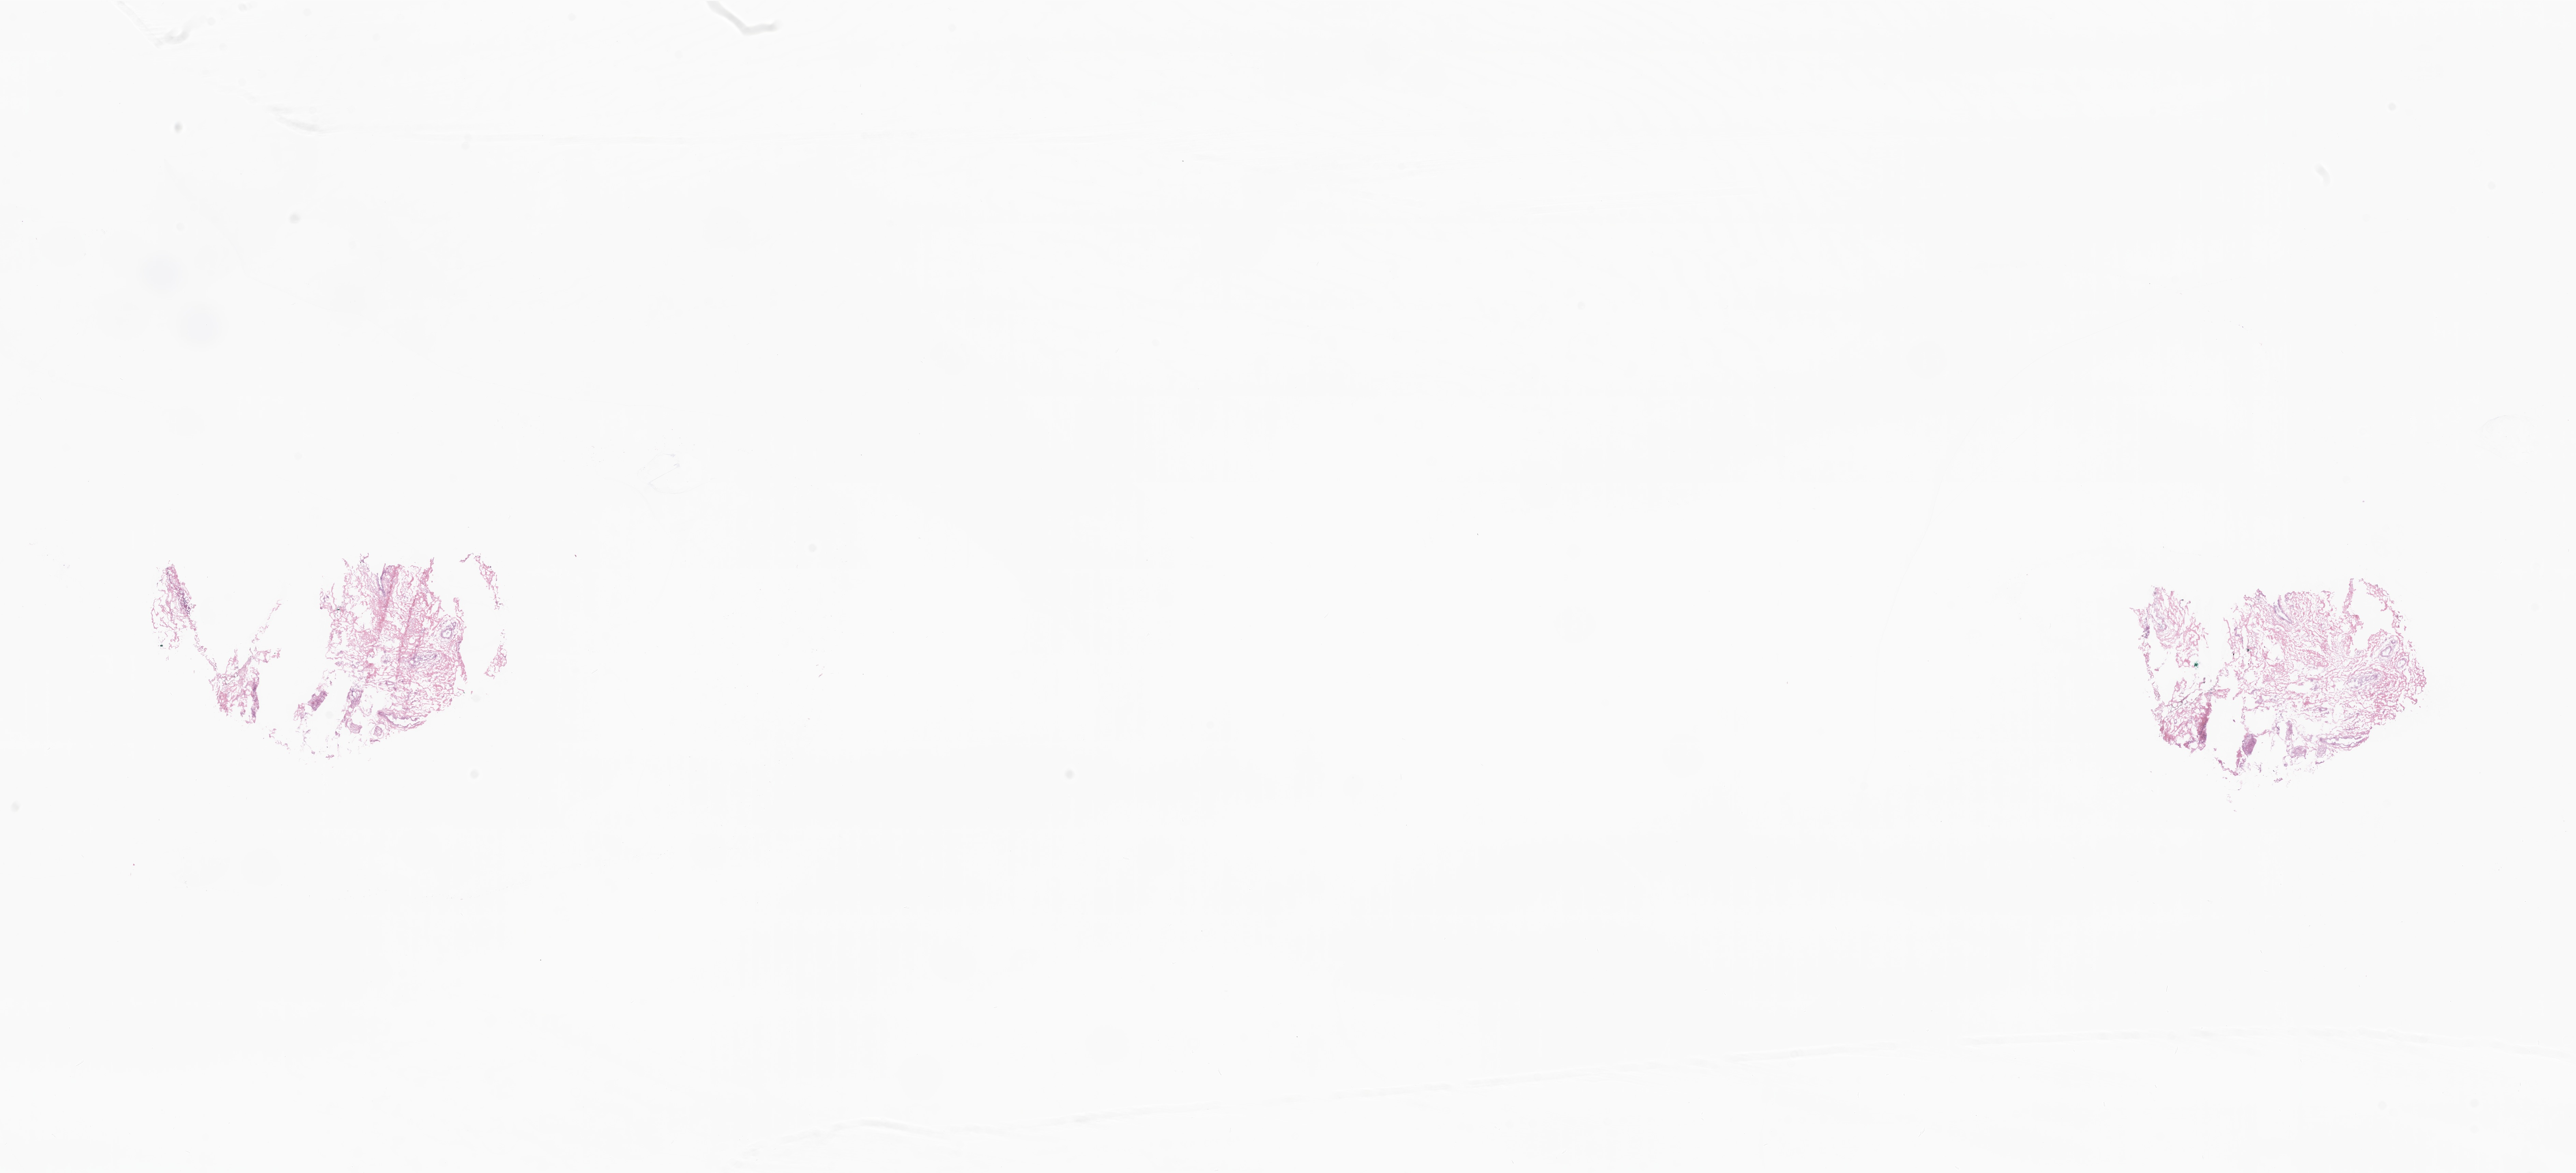
Digitized H&E-stained section — a low-resolution overview of the entire scanned area, about 31.8 x 14.5 mm; frozen section; primary tumor; anatomic site: breast (right). Female patient; age at initial diagnosis 79 years. Pathologist review of this section (percent, as recorded): tumor cells 0%, tumor nuclei 0%, stromal cells 5%, necrosis 0%, normal cells 95%. Inflammatory infiltration, as recorded: lymphocyte infiltration 0%, monocyte infiltration 0%, neutrophil infiltration 0%.
Diagnosis: Infiltrating duct carcinoma, NOS. Section: bottom of the tissue portion.